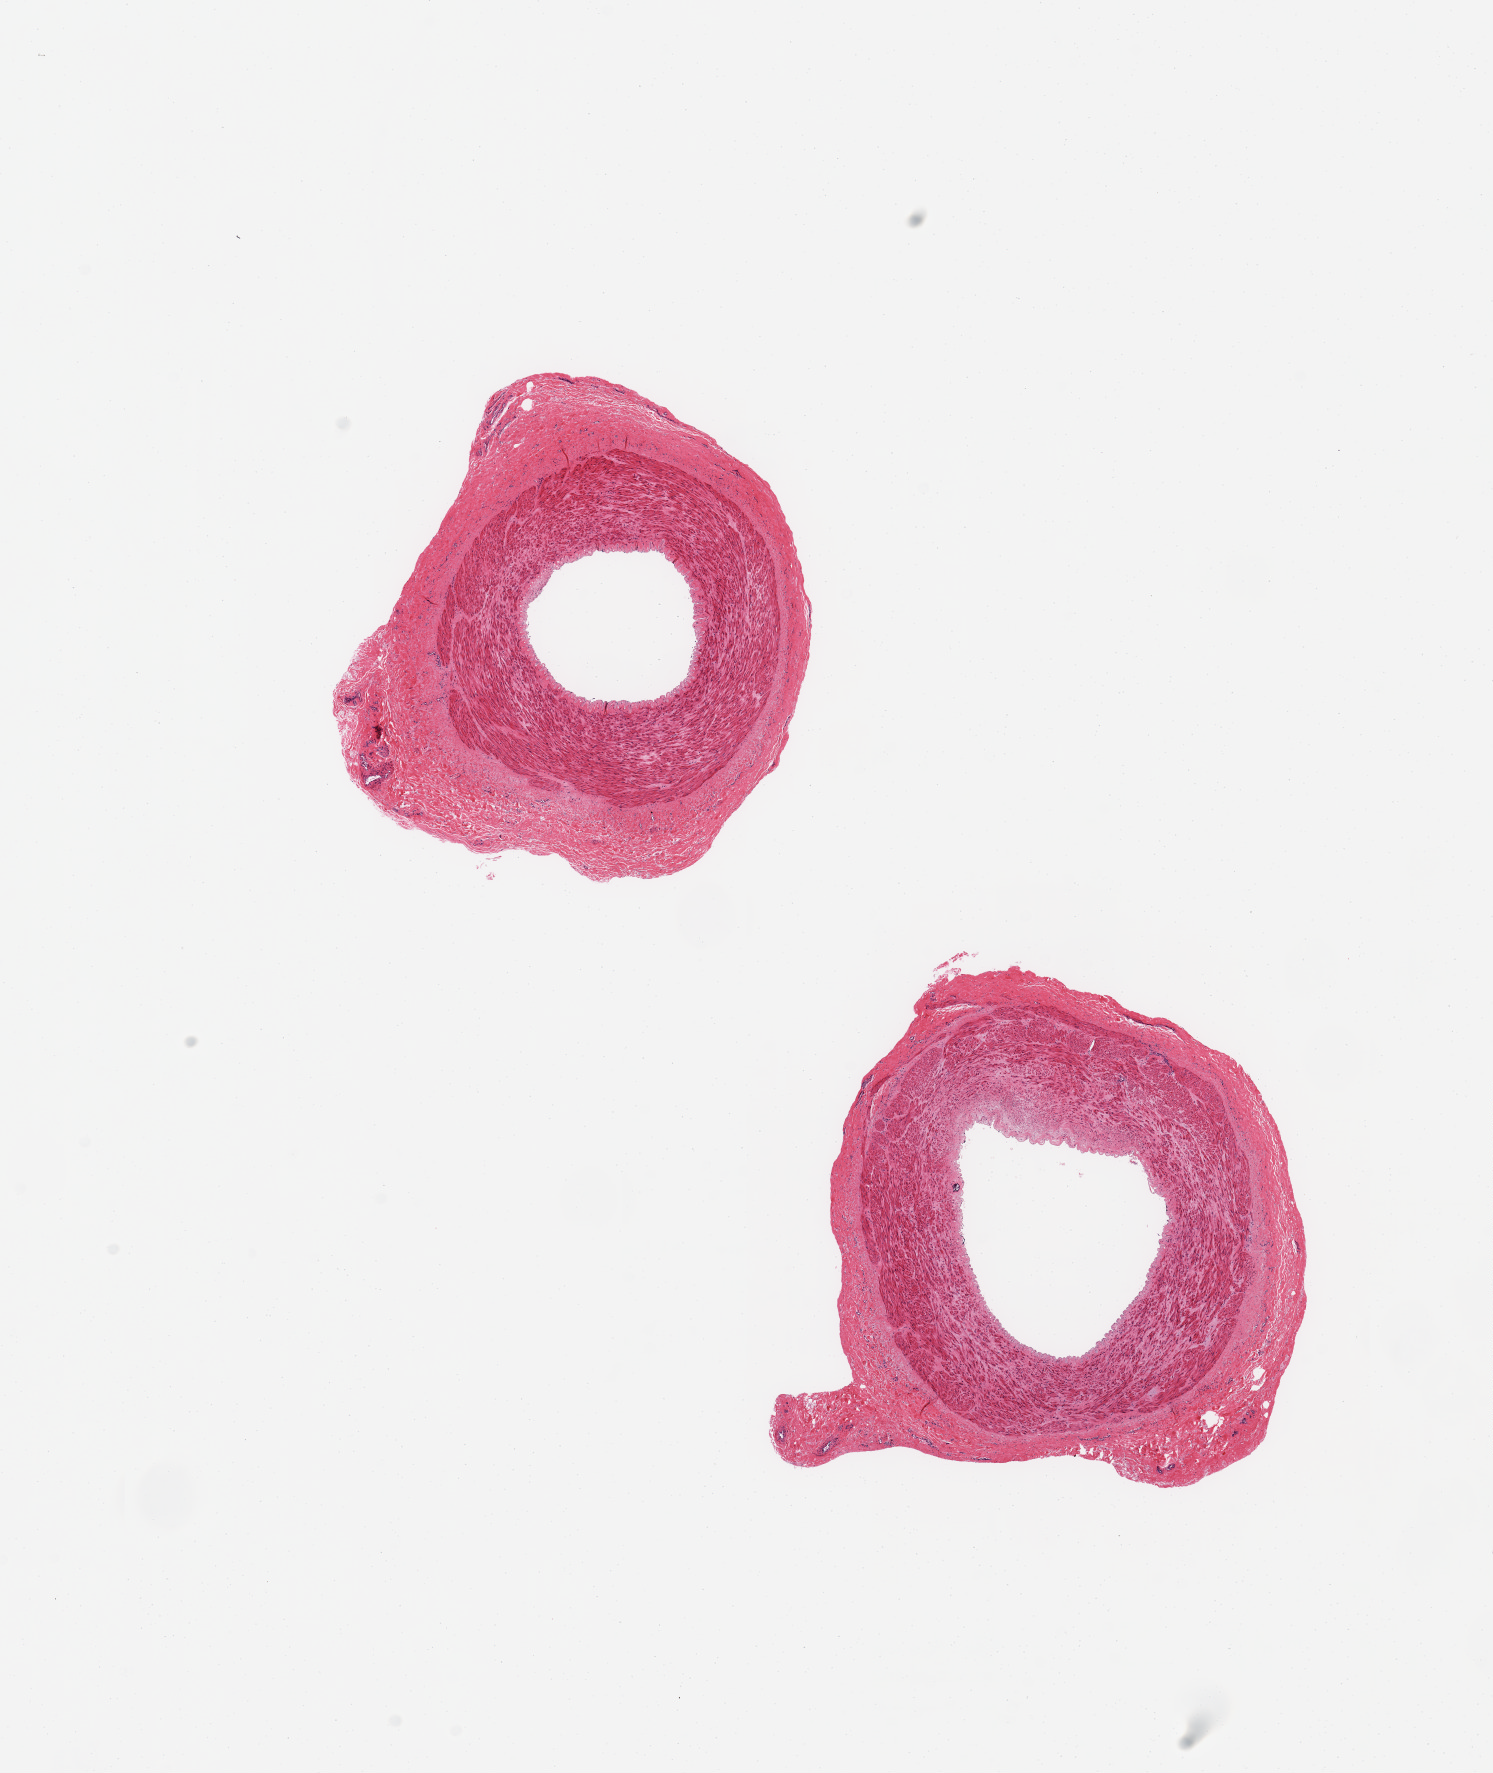
Whole-slide image, H&E stain — a low-resolution overview of the entire scanned area, about 11.8 x 14.0 mm, PAXgene-fixed paraffin-embedded (PFPE) section, sampled site (target tissue): tibial artery, tissue donor sample. Donor: male.
• reviewer comment on this tissue sample: 2 pieces; up to 1mm attached adventitia